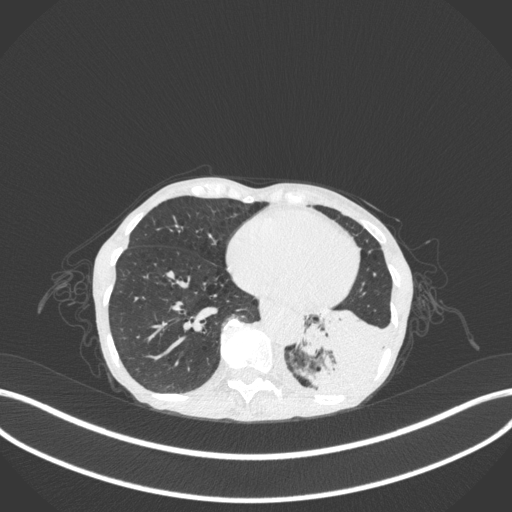
Chest CT, one axial slice; slice 73 of 347 in the series (ordered by position); reconstruction kernel B31f; 120 kVp; lung window (W 1500 / L -600 HU); 1 mm slice thickness; 512 × 512 image matrix. Female patient, age 70 years. Case-level facts recorded for this patient, not image findings: clinical TNM (as recorded): T3 N0 M0.
Outlined on this slice (bounding box drawn by a radiologist):
- lung tumour (recorded histology: small cell carcinoma): bounding box <296,296,390,407> (left, top, right, bottom; pixels)